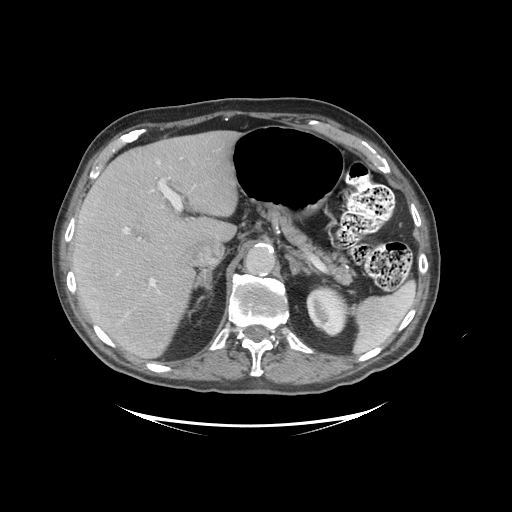
Contrast-enhanced abdominal CT (liver protocol), one axial slice; slice 66 of 99 in the series (ordered by position); reconstruction kernel STANDARD; soft-tissue window (W 400 / L 40 HU); 2.5 mm slice thickness; 512 × 512 image matrix. Case-level facts recorded for this patient, not image findings: diagnosis: hepatocellular carcinoma (patient treated with transarterial chemoembolisation; whether this scan precedes or follows treatment is not stated here); TNM stage (as recorded): Stage-I; Child-Pugh class: A; tumour differentiation: moderately differentiated.
Outlined on this slice (semi-automatic segmentation, software-assisted and operator-edited):
- liver parenchyma outside the tumour (the mass and vessels are separate outlines, so this box may not span the whole liver): bounding box [x1, y1, x2, y2] px = [72, 130, 238, 358]
- liver vessels: [123, 161, 166, 316]